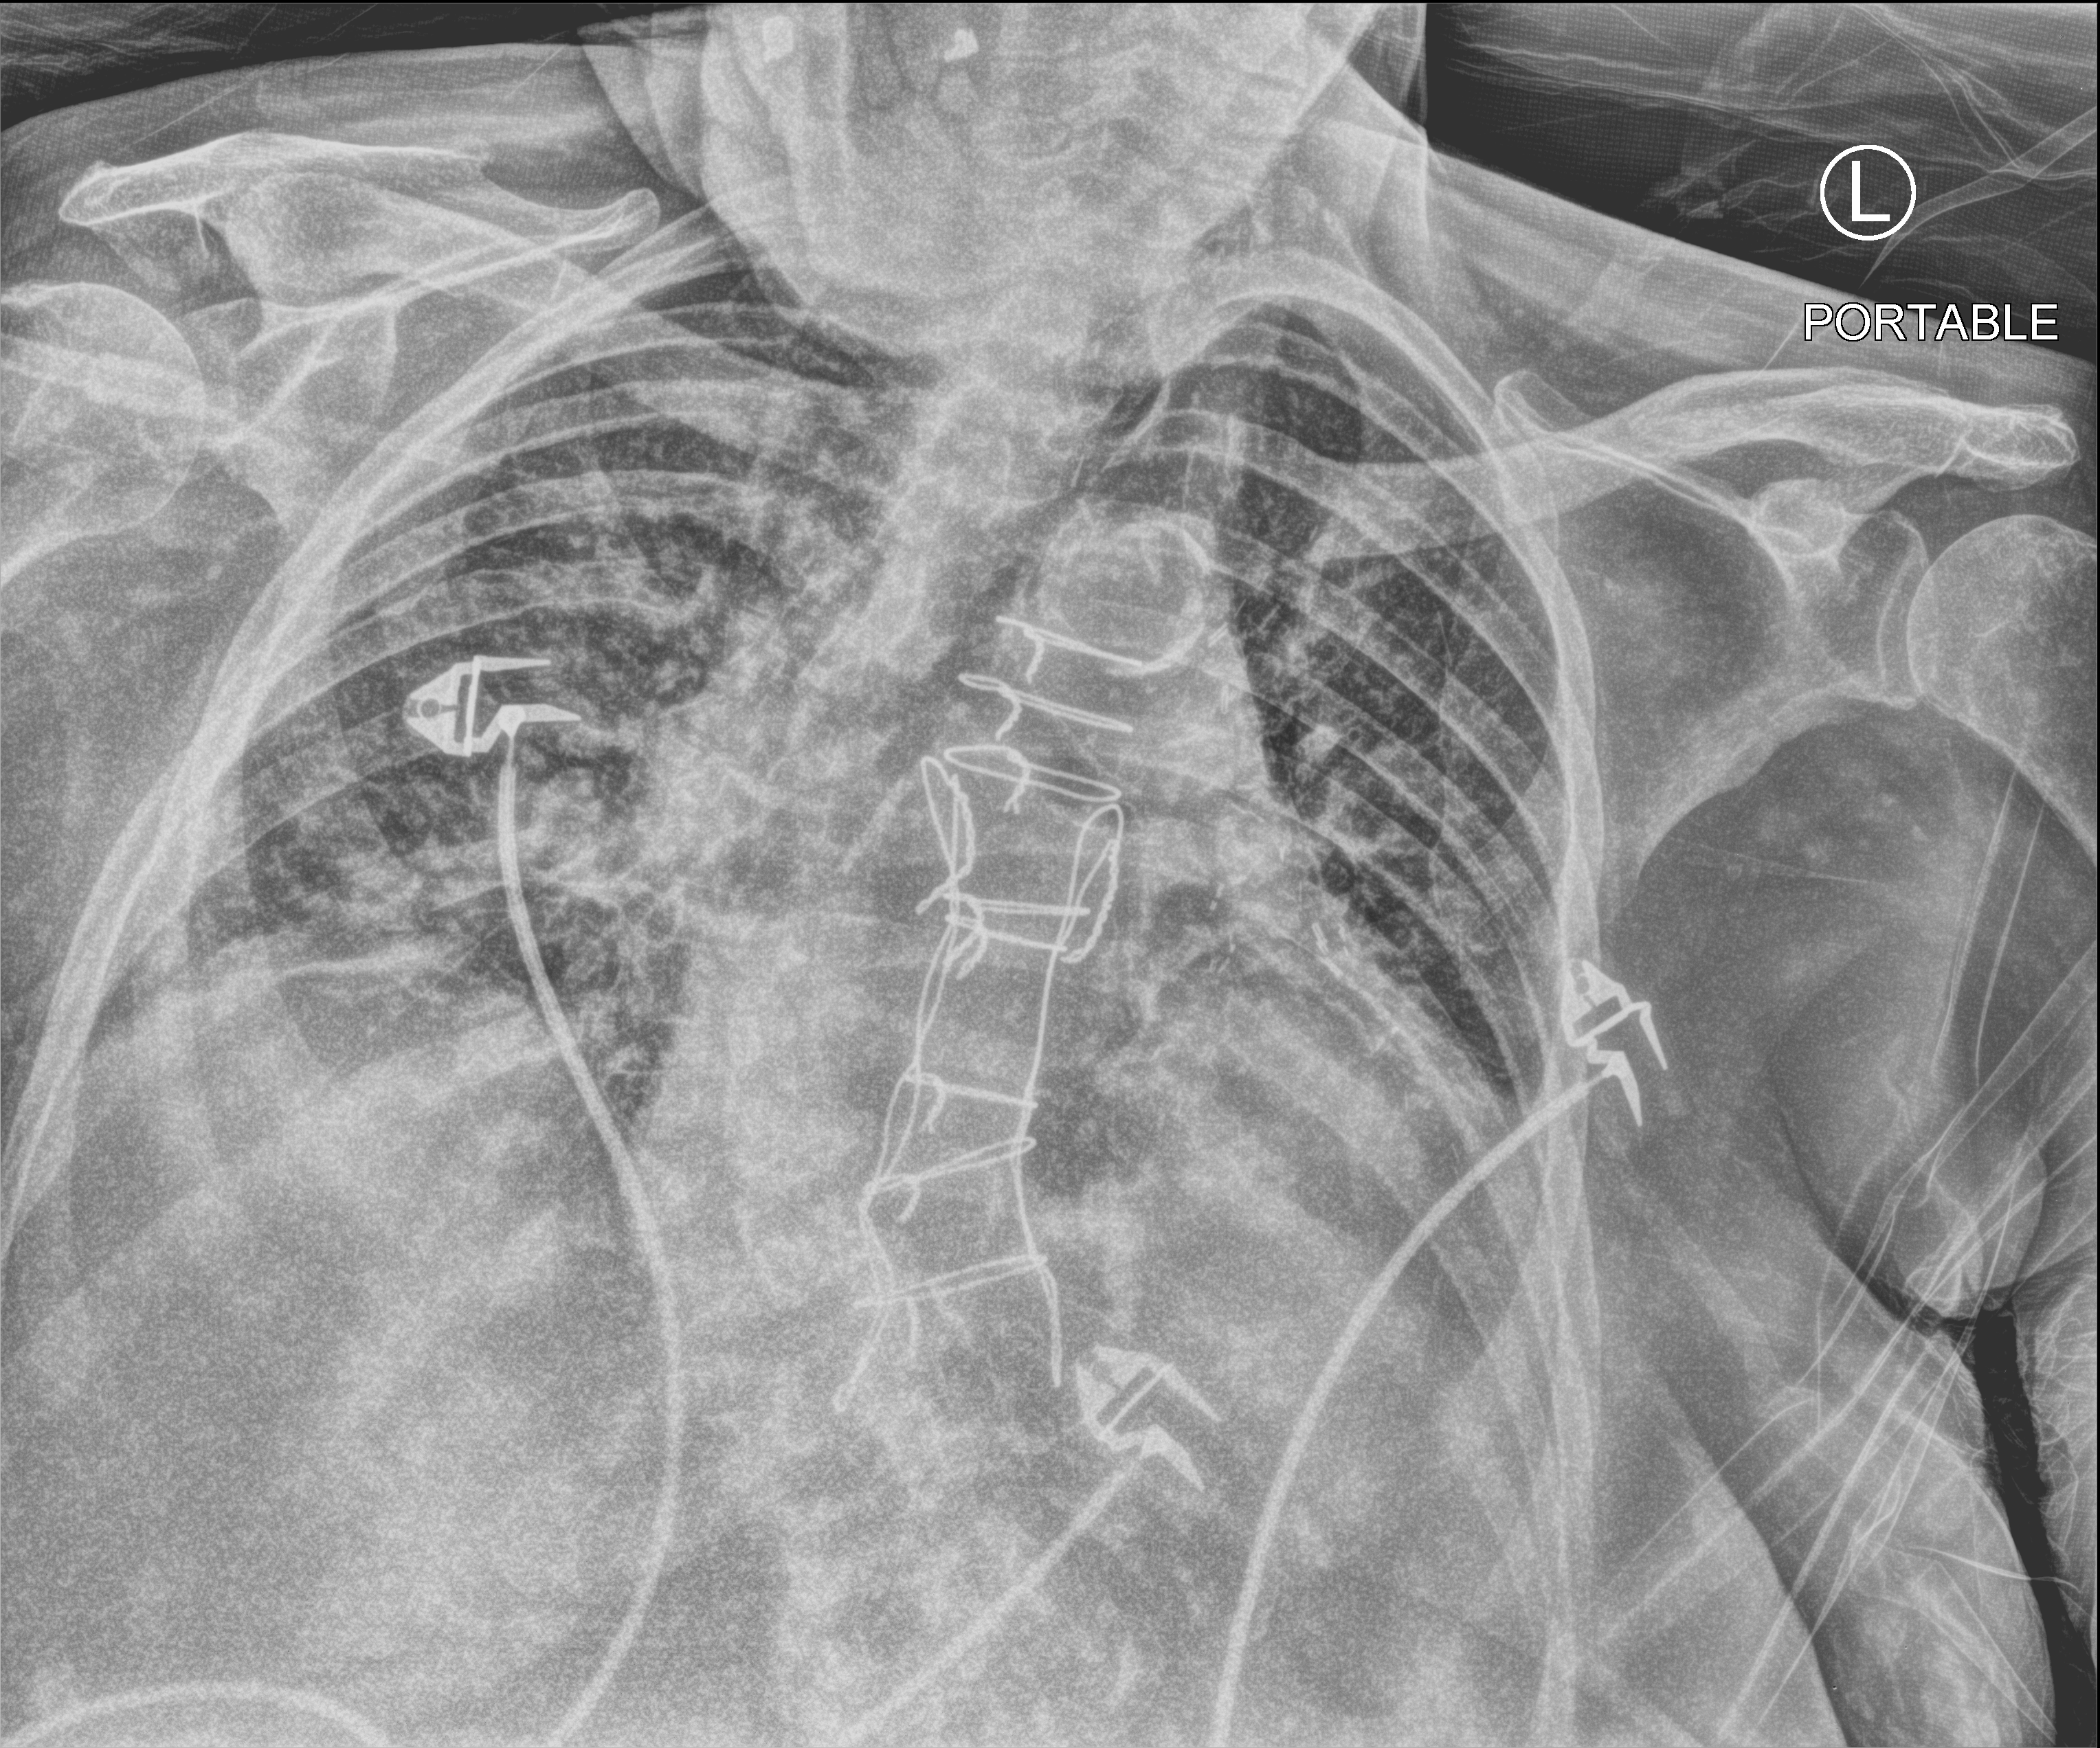
Chest X-ray (portable), anteroposterior (AP) projection. Female patient hospitalised with COVID-19, age 75–90 years.
Admission-level facts for this patient (not findings on this image; timing relative to this image not recorded):
- mechanically ventilated during this hospital stay: no
- length of hospital stay: 10 days